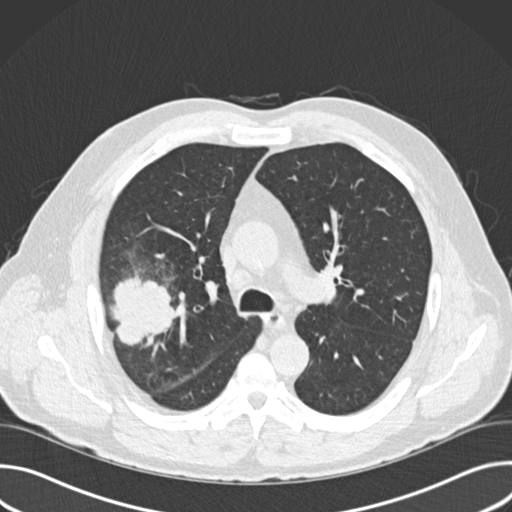
Low-dose screening chest CT, one axial slice; slice 107 of 157 in the series (ordered by position); reconstruction kernel B30f; 120 kVp; lung window (W 1500 / L -600 HU); 2 mm slice thickness; 512 × 512 image matrix, field of view 380 × 380 mm.
Outlined on this slice (outlined manually by an expert reader):
- lesion 1 (tumor, upper lobe of right lung): bounding box [x1, y1, x2, y2] px = [110, 273, 177, 346]